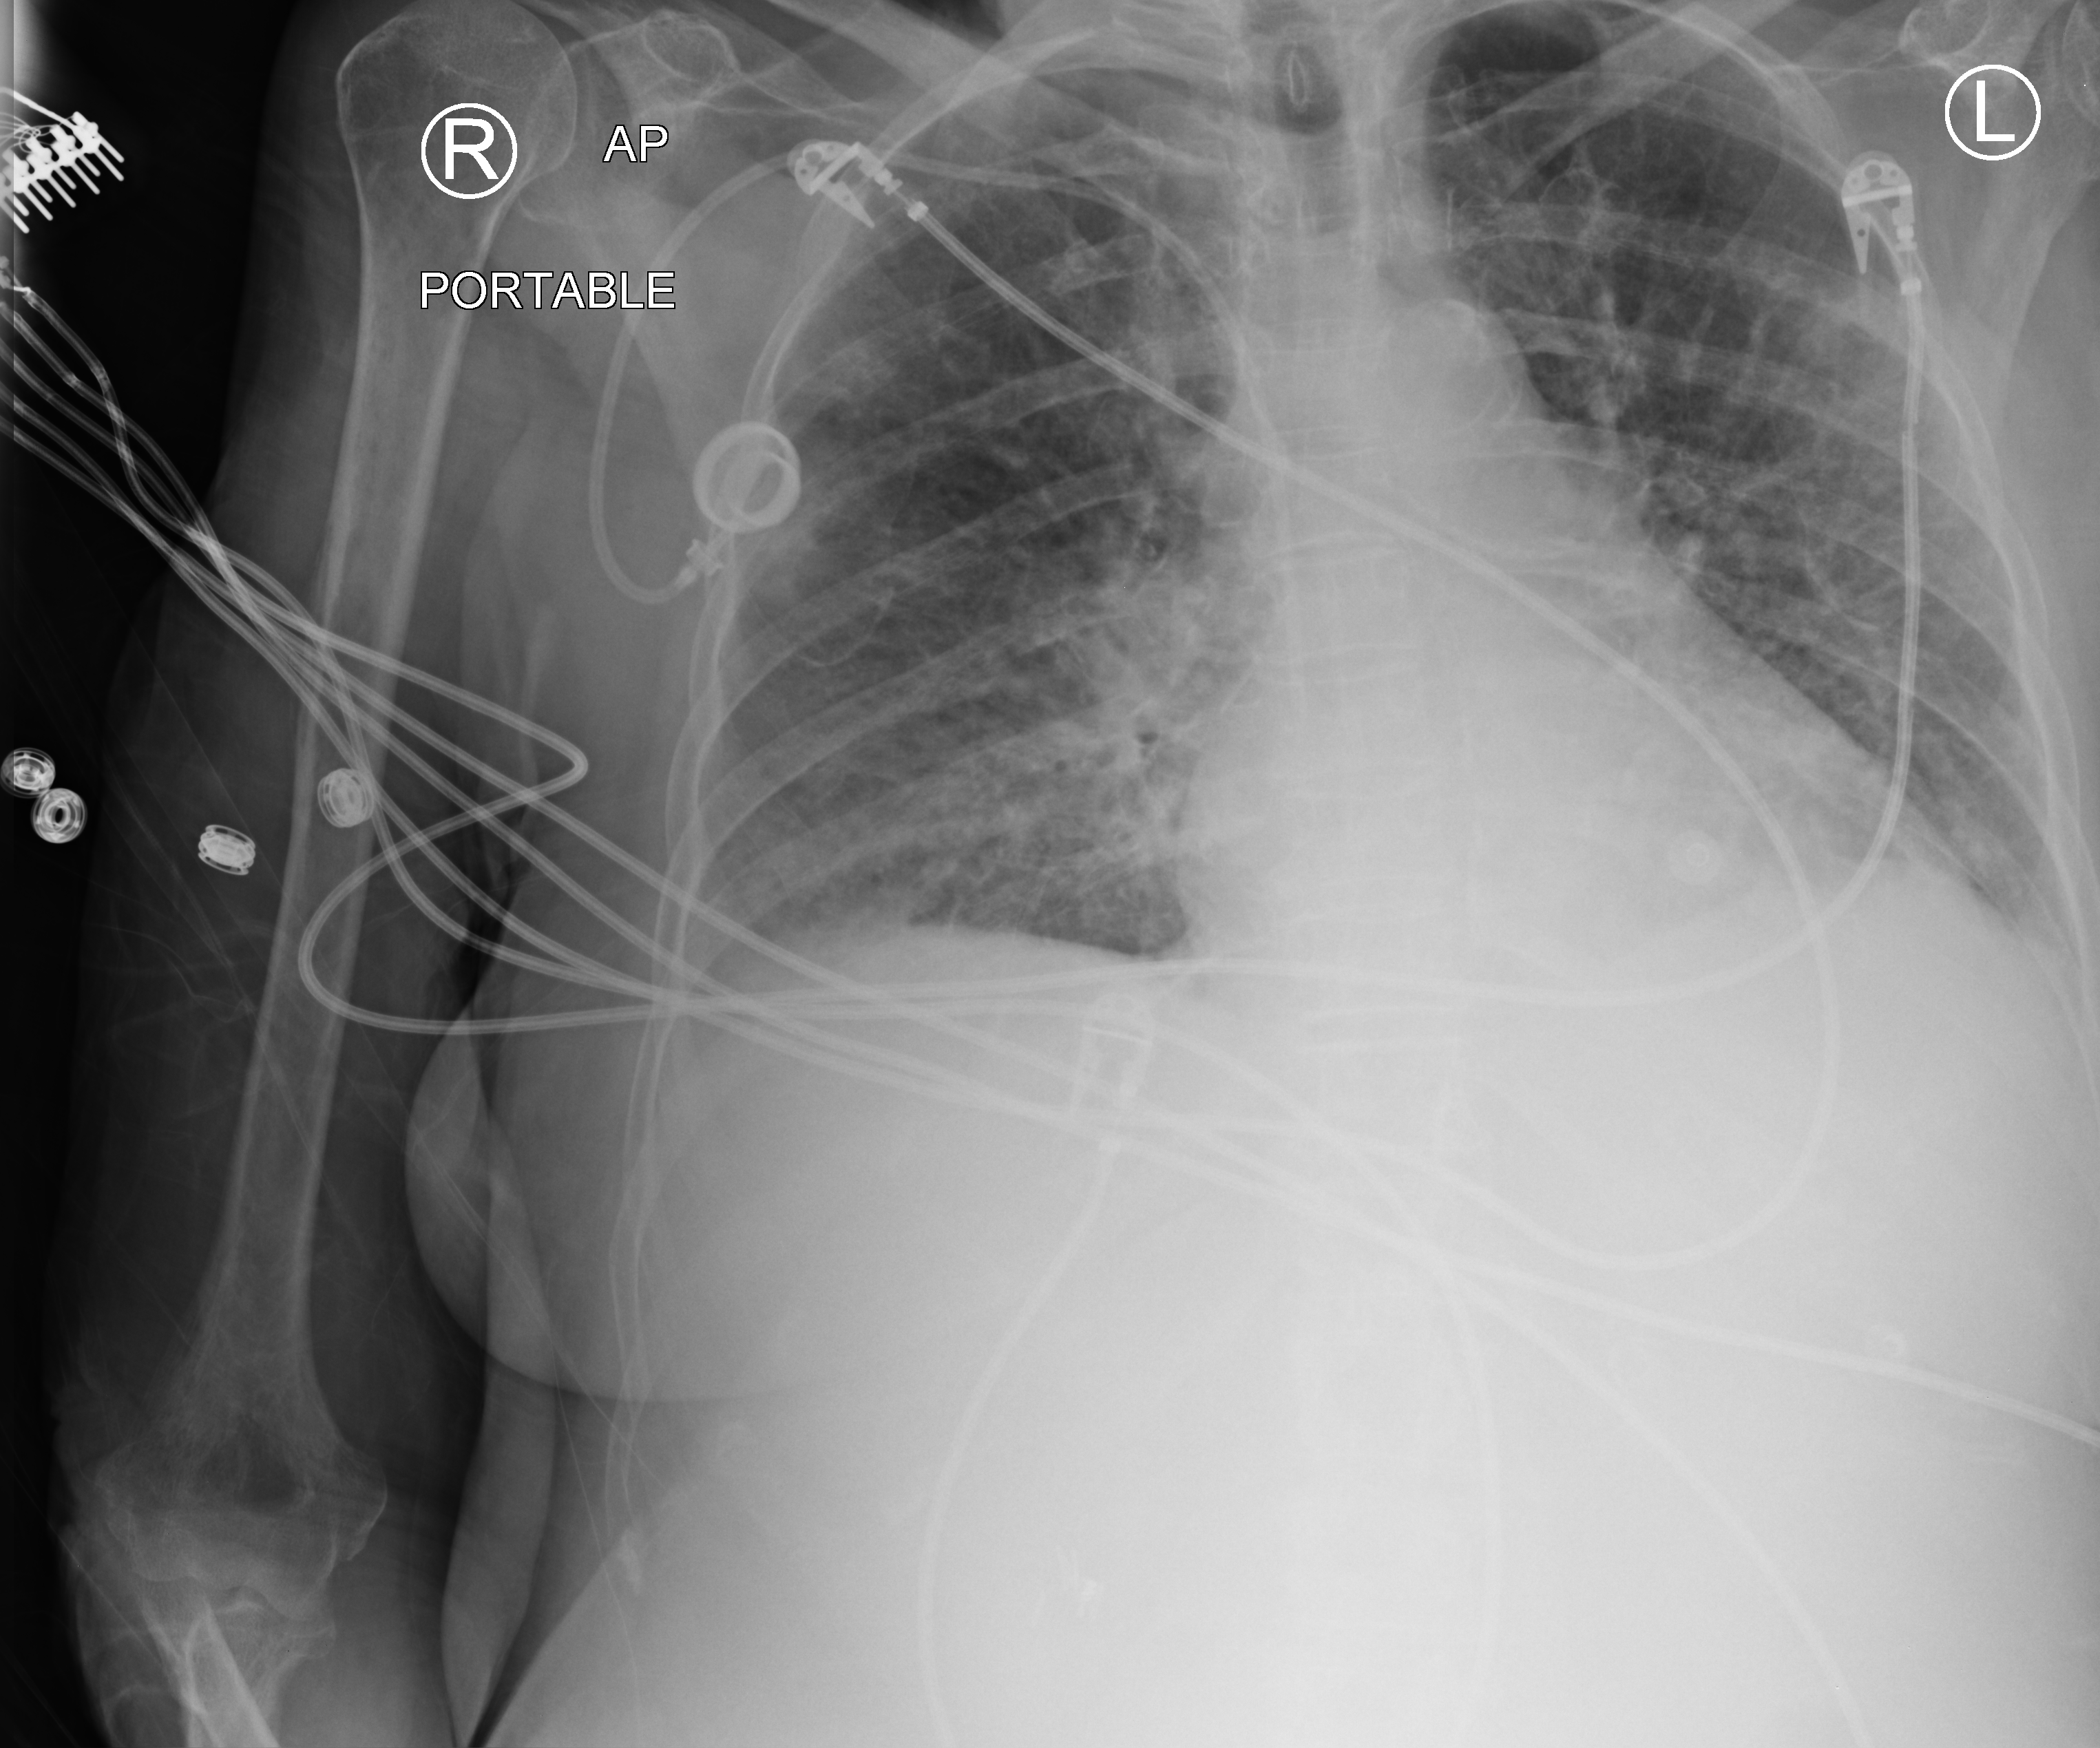
Portable chest radiograph. Female patient hospitalised with COVID-19, age 75–90 years.
From the hospital-stay record, not from the radiograph (when in the stay this image was taken is not recorded): length of hospital stay: 7 days.